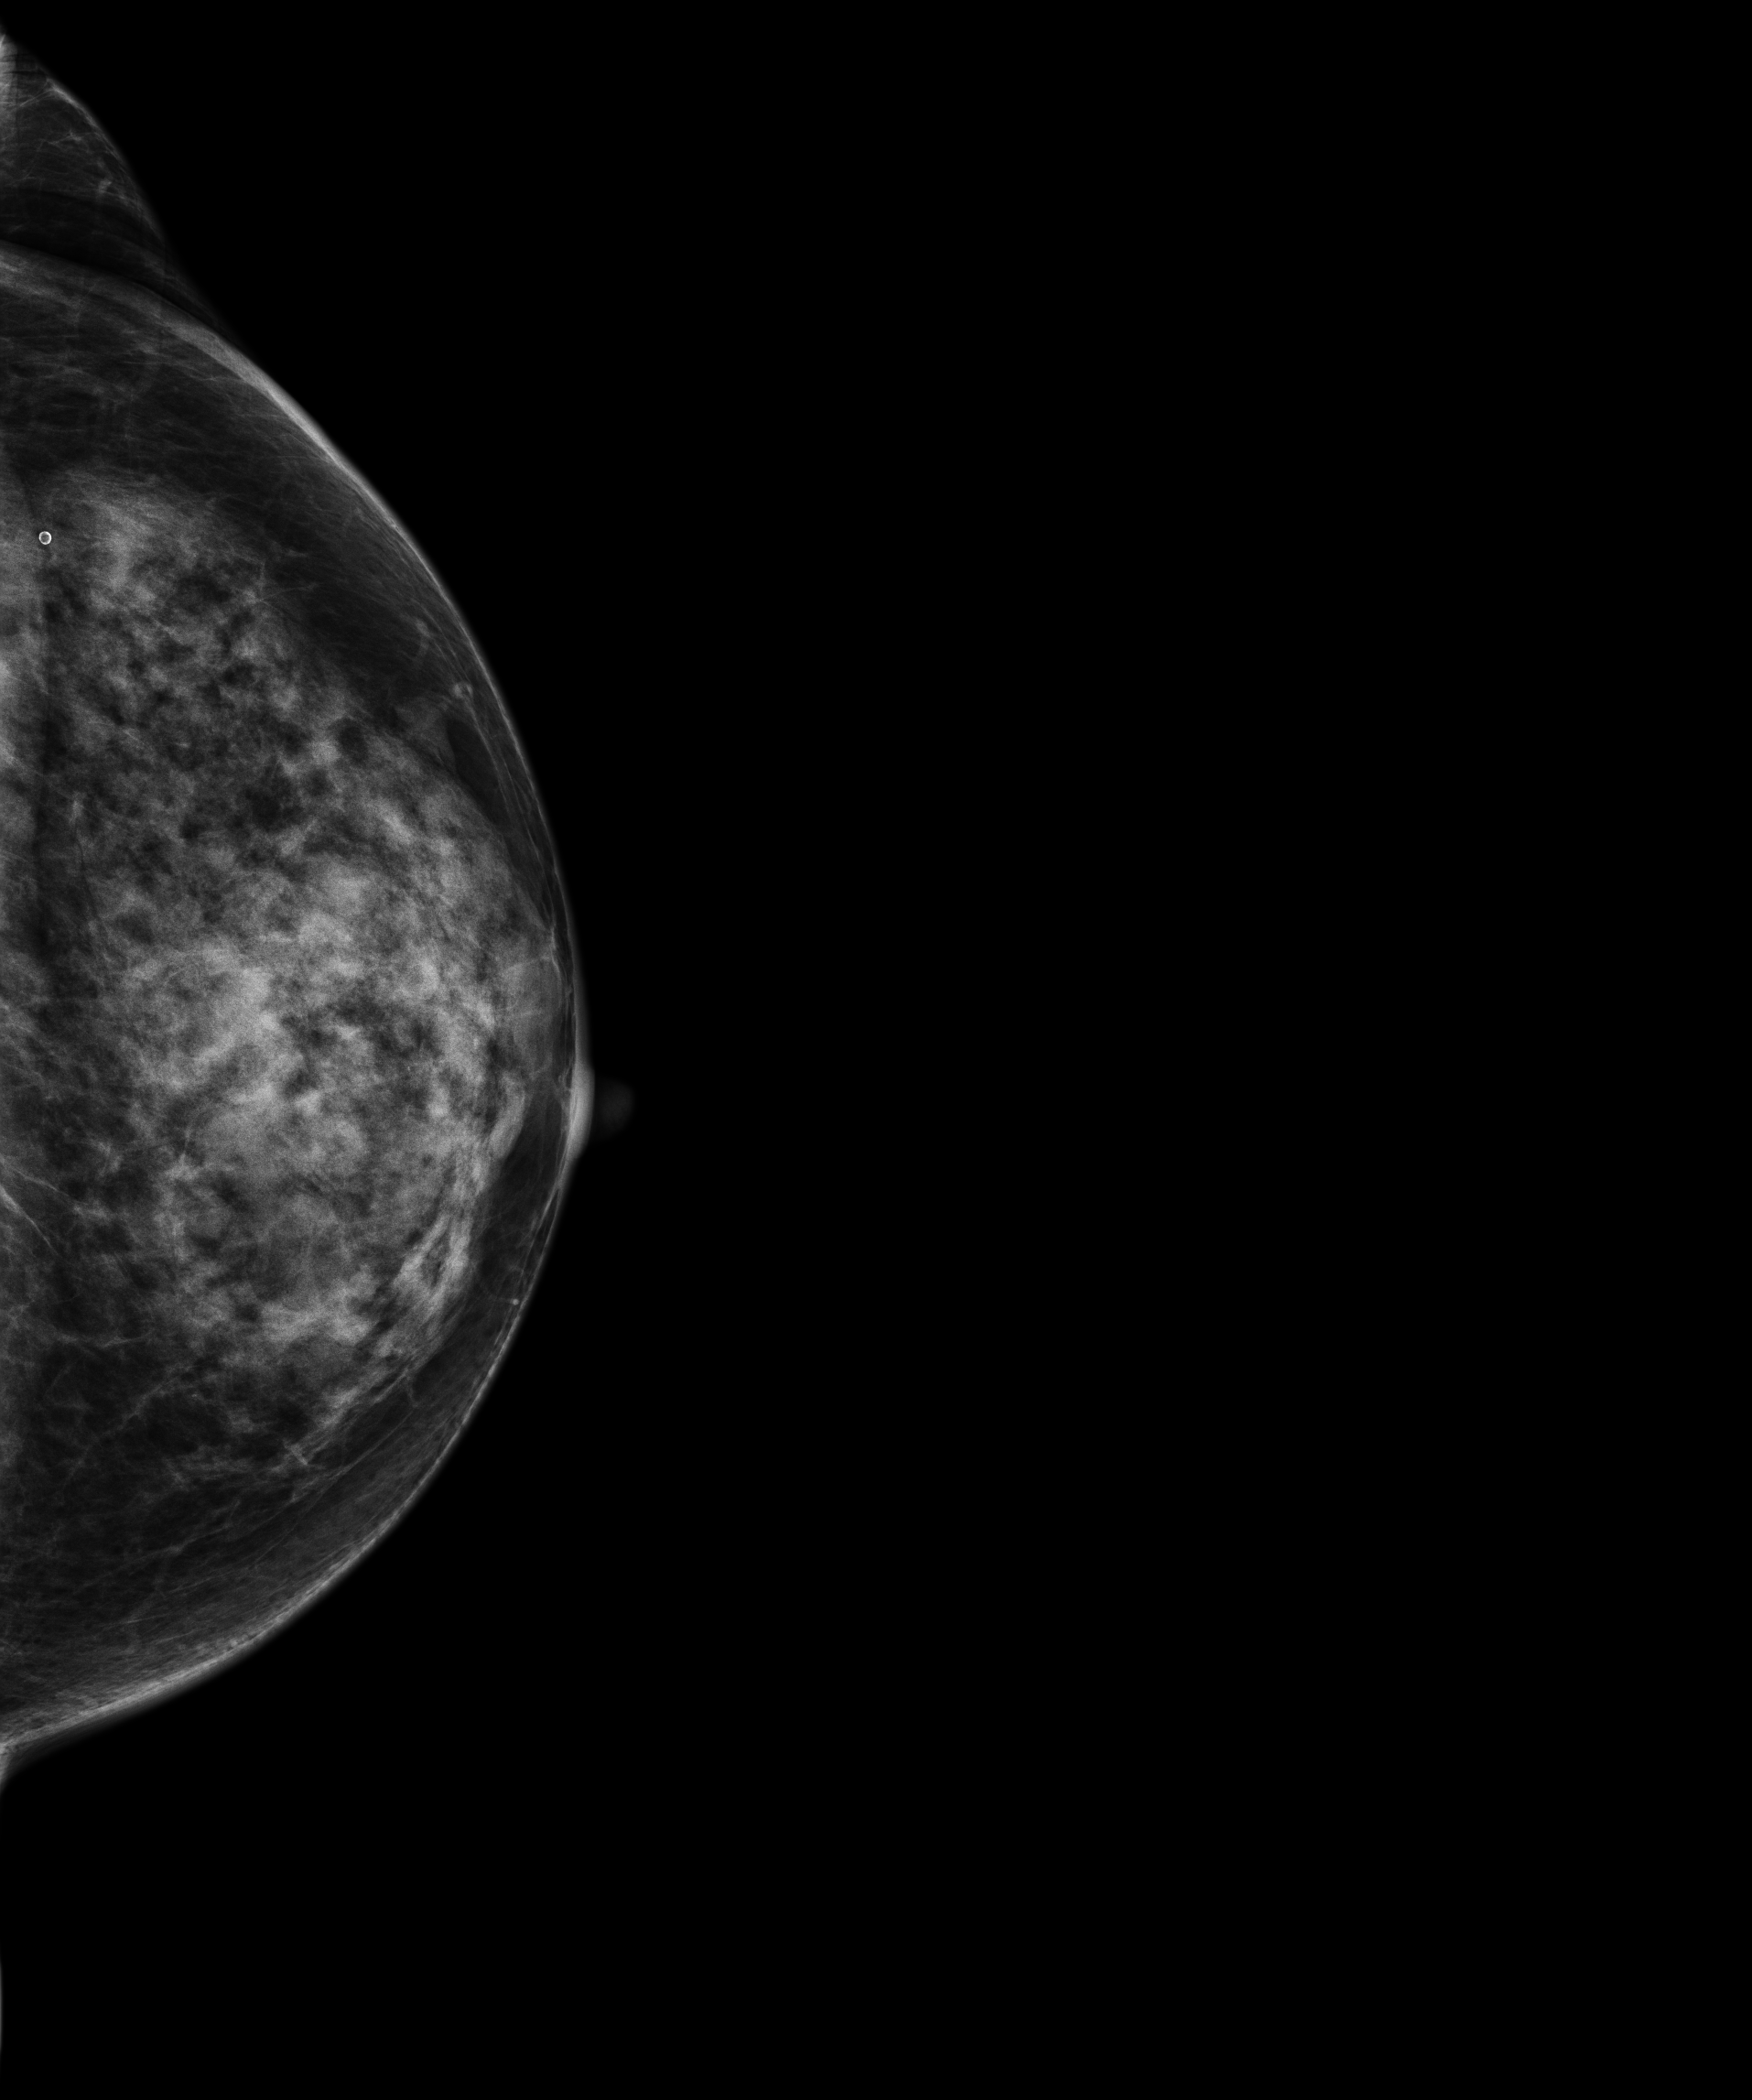
Full-field digital mammogram (FFDM); left breast; CC view; annual screening mammography examination; compressed breast thickness 39 mm. Female patient, age 67 years.
Final BI-RADS category for the screening round (tomosynthesis exam, both breasts): category 1.